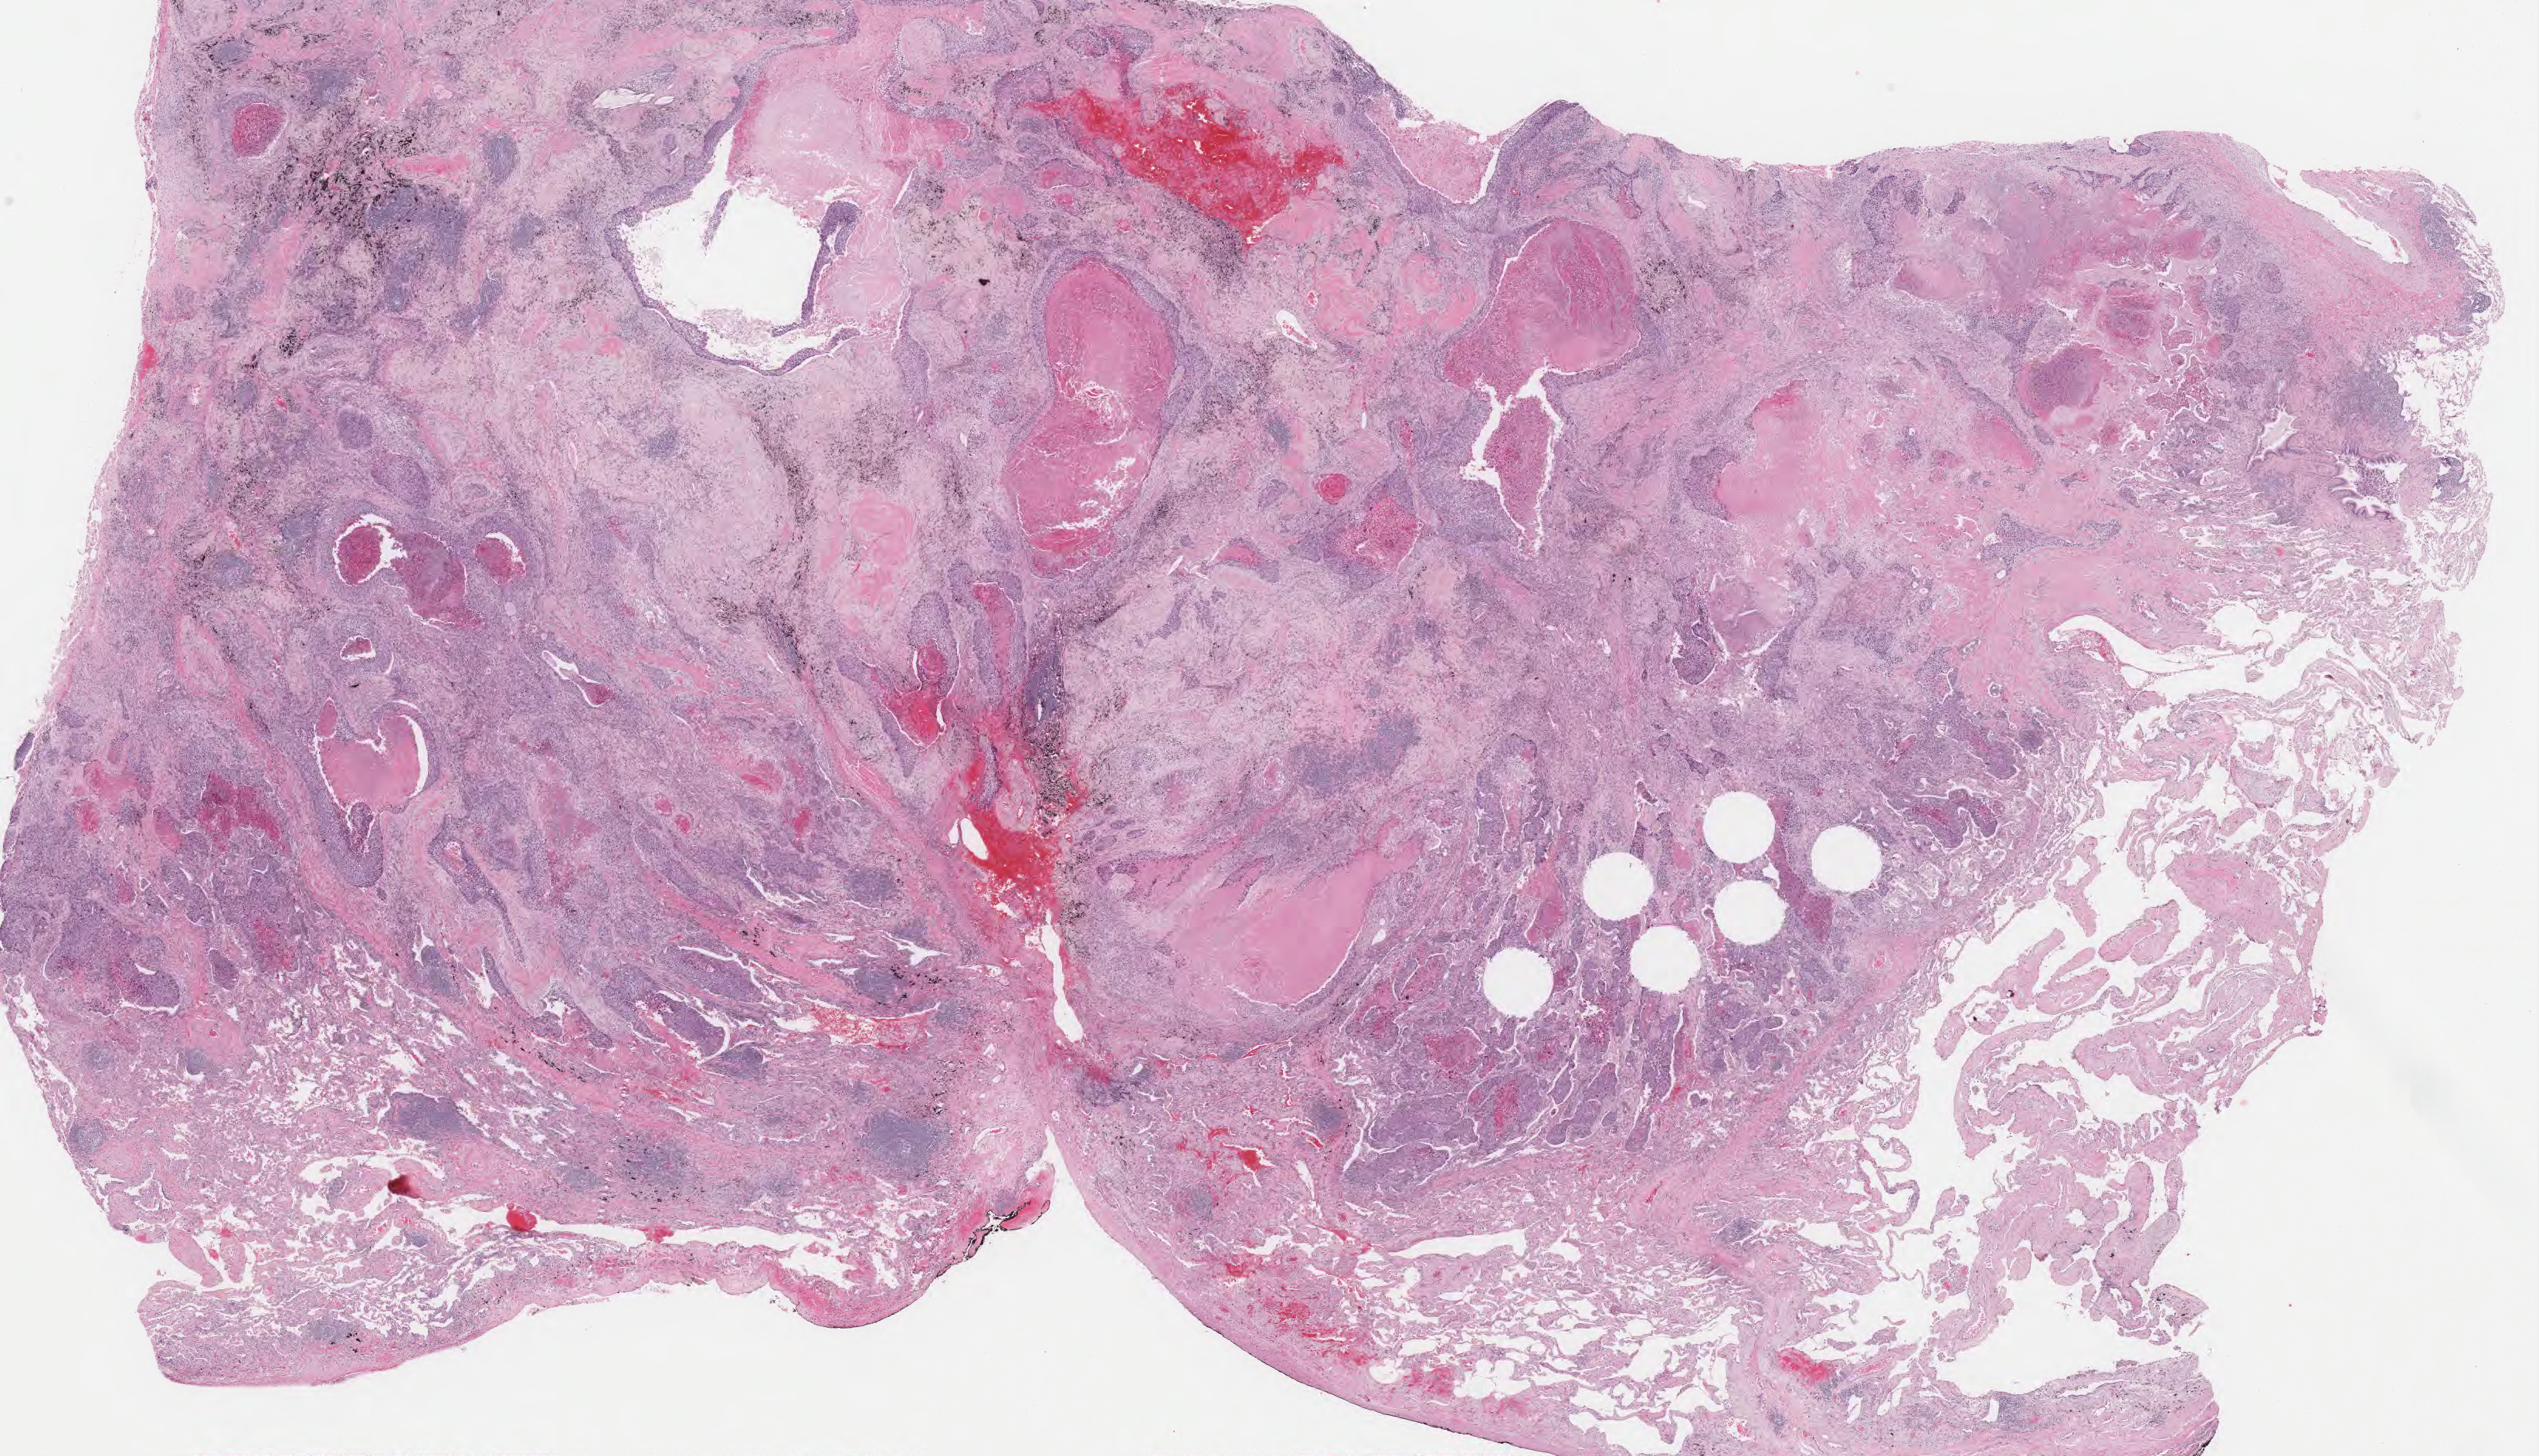
Digitized H&E-stained tissue section (whole slide) — a low-resolution overview of the entire scanned area, about 26.3 x 15.1 mm, formalin-fixed paraffin-embedded (FFPE) diagnostic section, primary tumour sample from the lung. Patient: male, age at initial diagnosis 70 years.
Pathologic diagnosis: Squamous cell carcinoma, NOS (upper lobe, lung). Laterality: right. AJCC pathologic stage: IB.